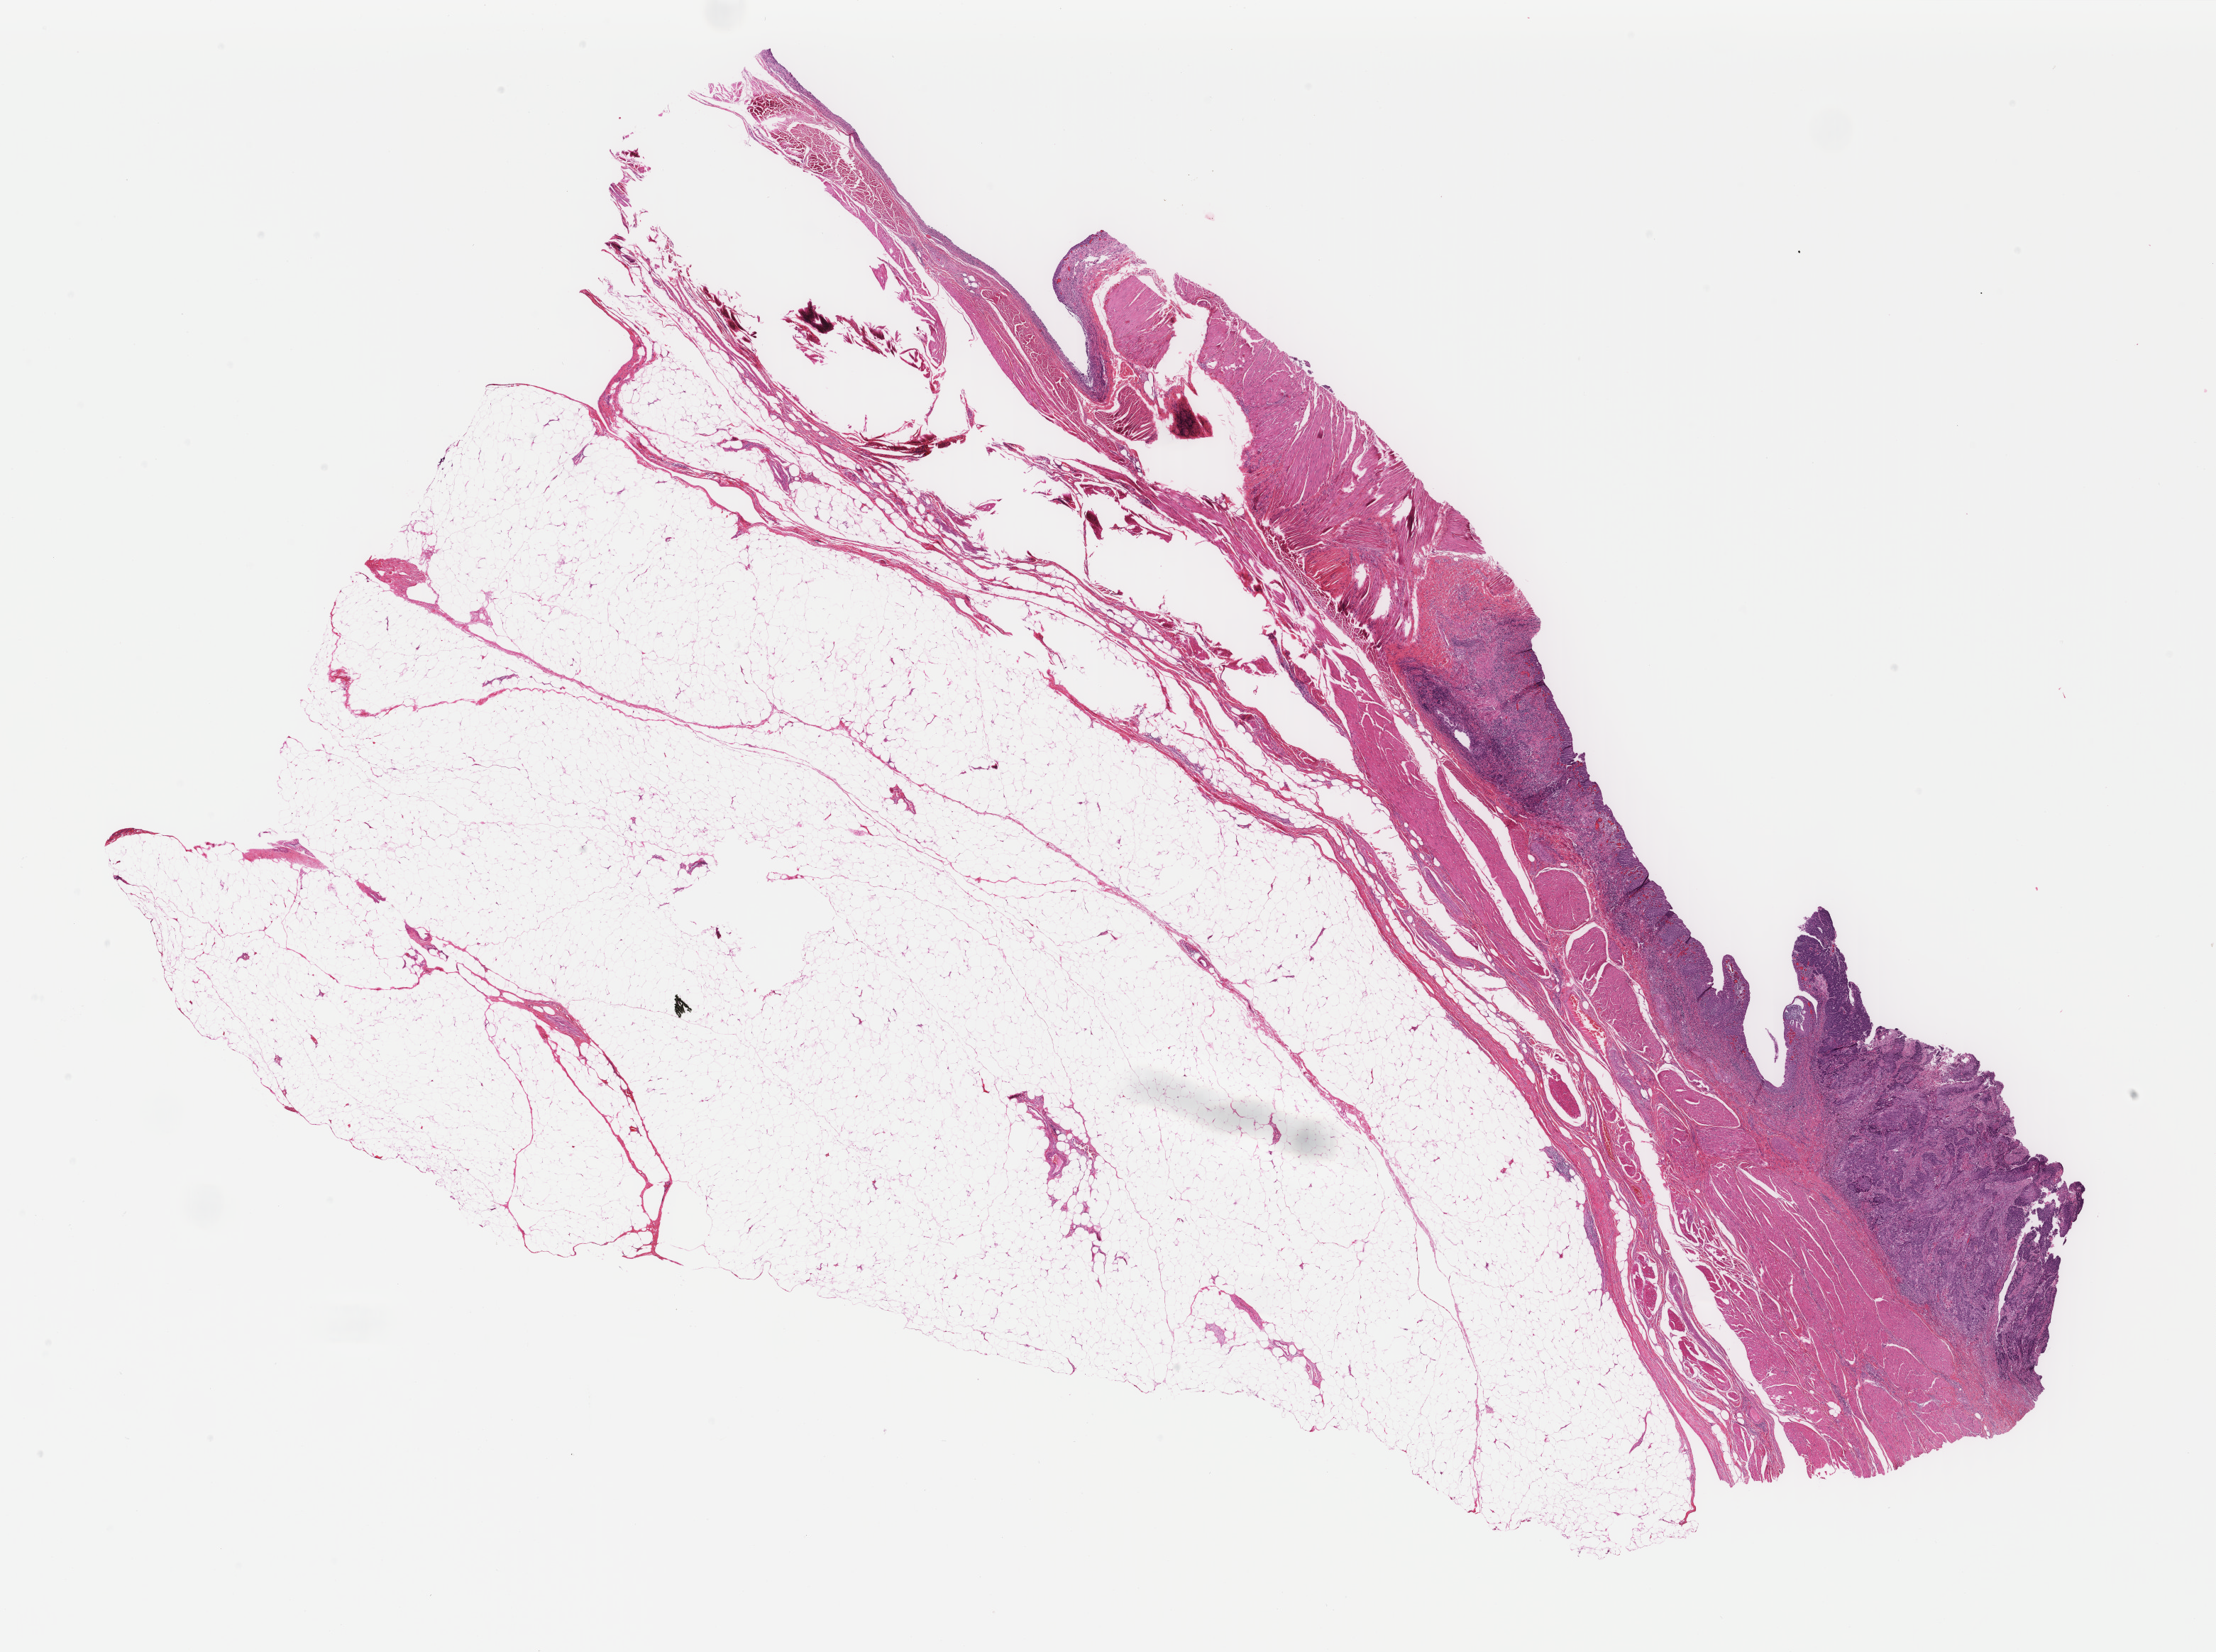
H&E-stained whole-slide image, low-resolution overview of the scanned area, about 24.8 x 18.5 mm (acquisition: 40x scan); formalin-fixed paraffin-embedded (FFPE) diagnostic section; sample: primary tumour, bladder. Male patient; age at initial diagnosis 85 years. Histologic grade: high grade.
• AJCC pathologic stage: II (6th edition)
• diagnosis: Transitional cell carcinoma